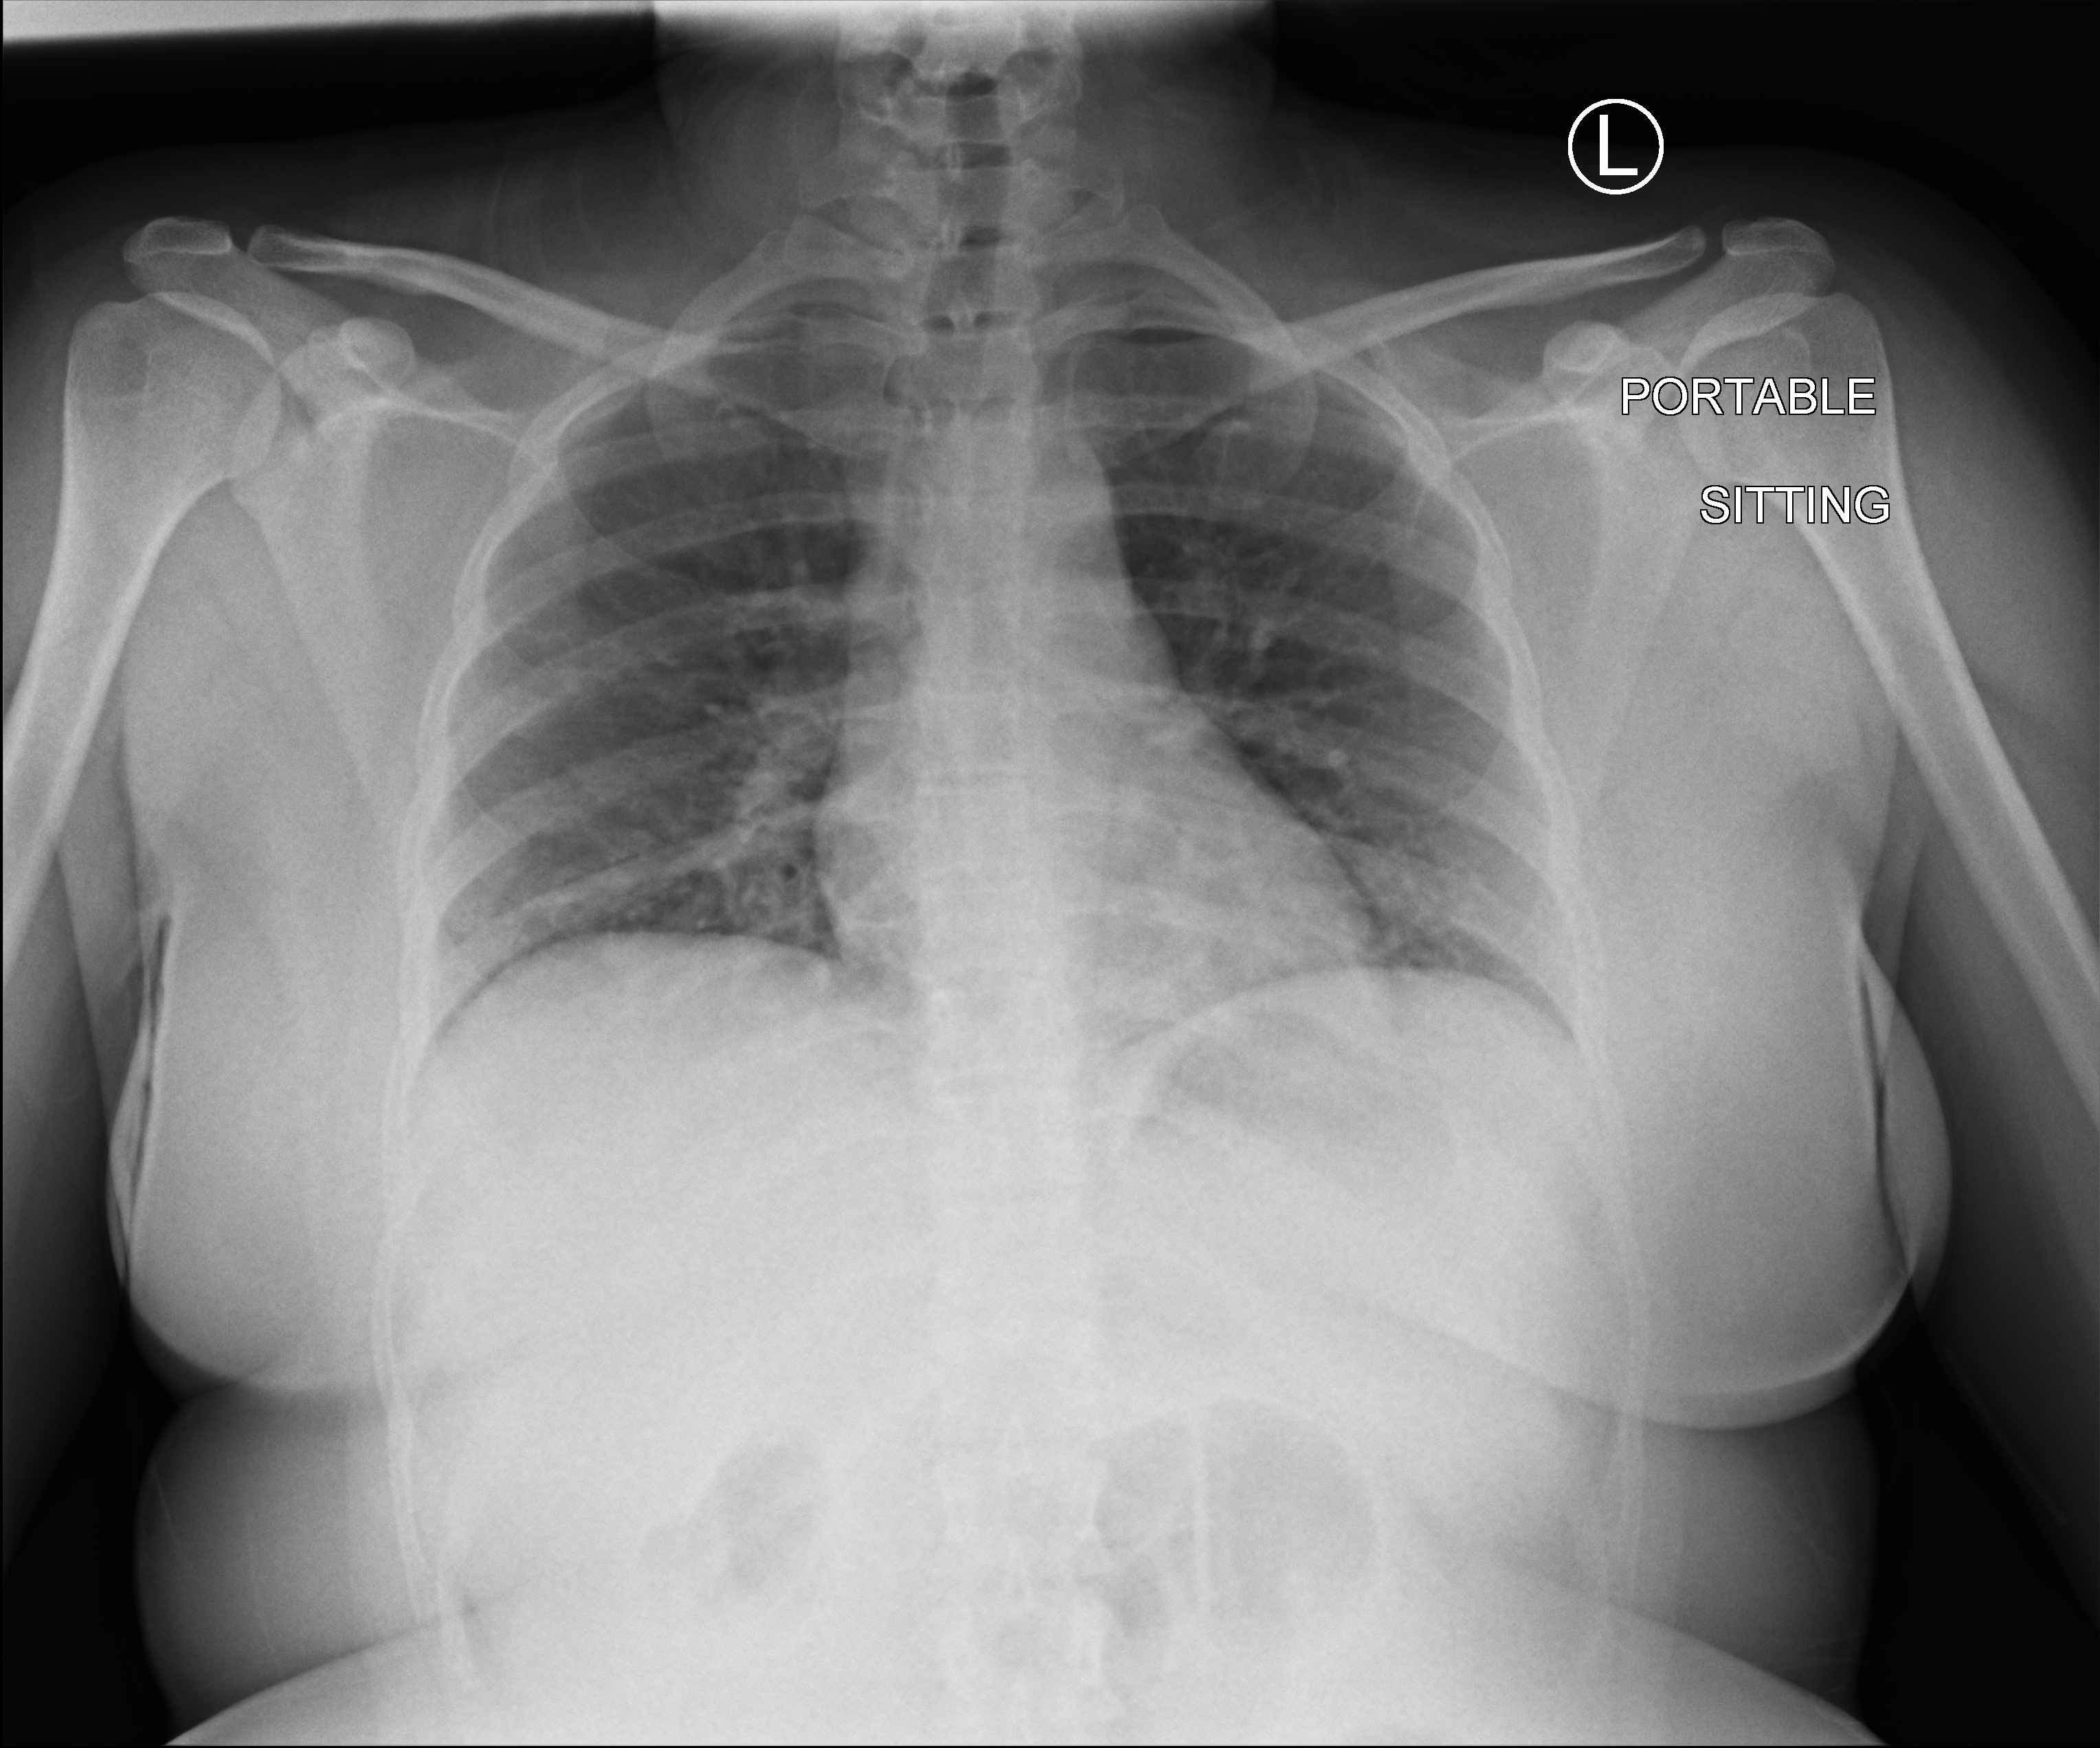
Portable chest radiograph; anteroposterior (AP) projection. Female patient hospitalised with COVID-19, age 18–59 years.
Admission-level facts for this patient (not findings on this image; timing relative to this image not recorded):
- mechanically ventilated during this hospital stay: no
- hypertension (admission record): no